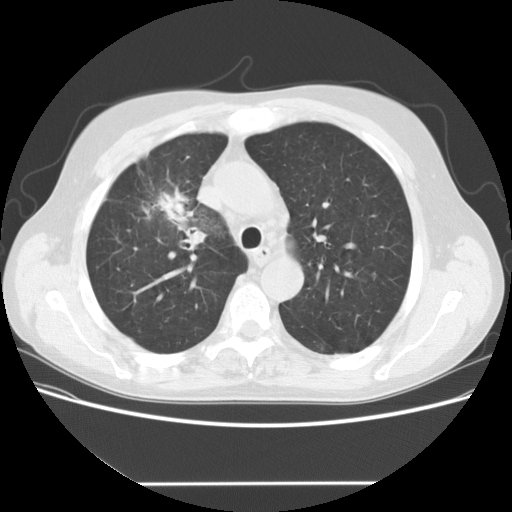
Low-dose screening chest CT, one axial slice; position 110 of 153 along the scan axis; 120 kVp; lung window (W 1500 / L -600 HU); 512 × 512 image matrix.
Annotated regions visible in this slice (manually delineated by an expert):
- lesion 1 (tumor, upper lobe of right lung): bounding box (x1, y1, x2, y2) in pixels: (156, 192, 191, 221)